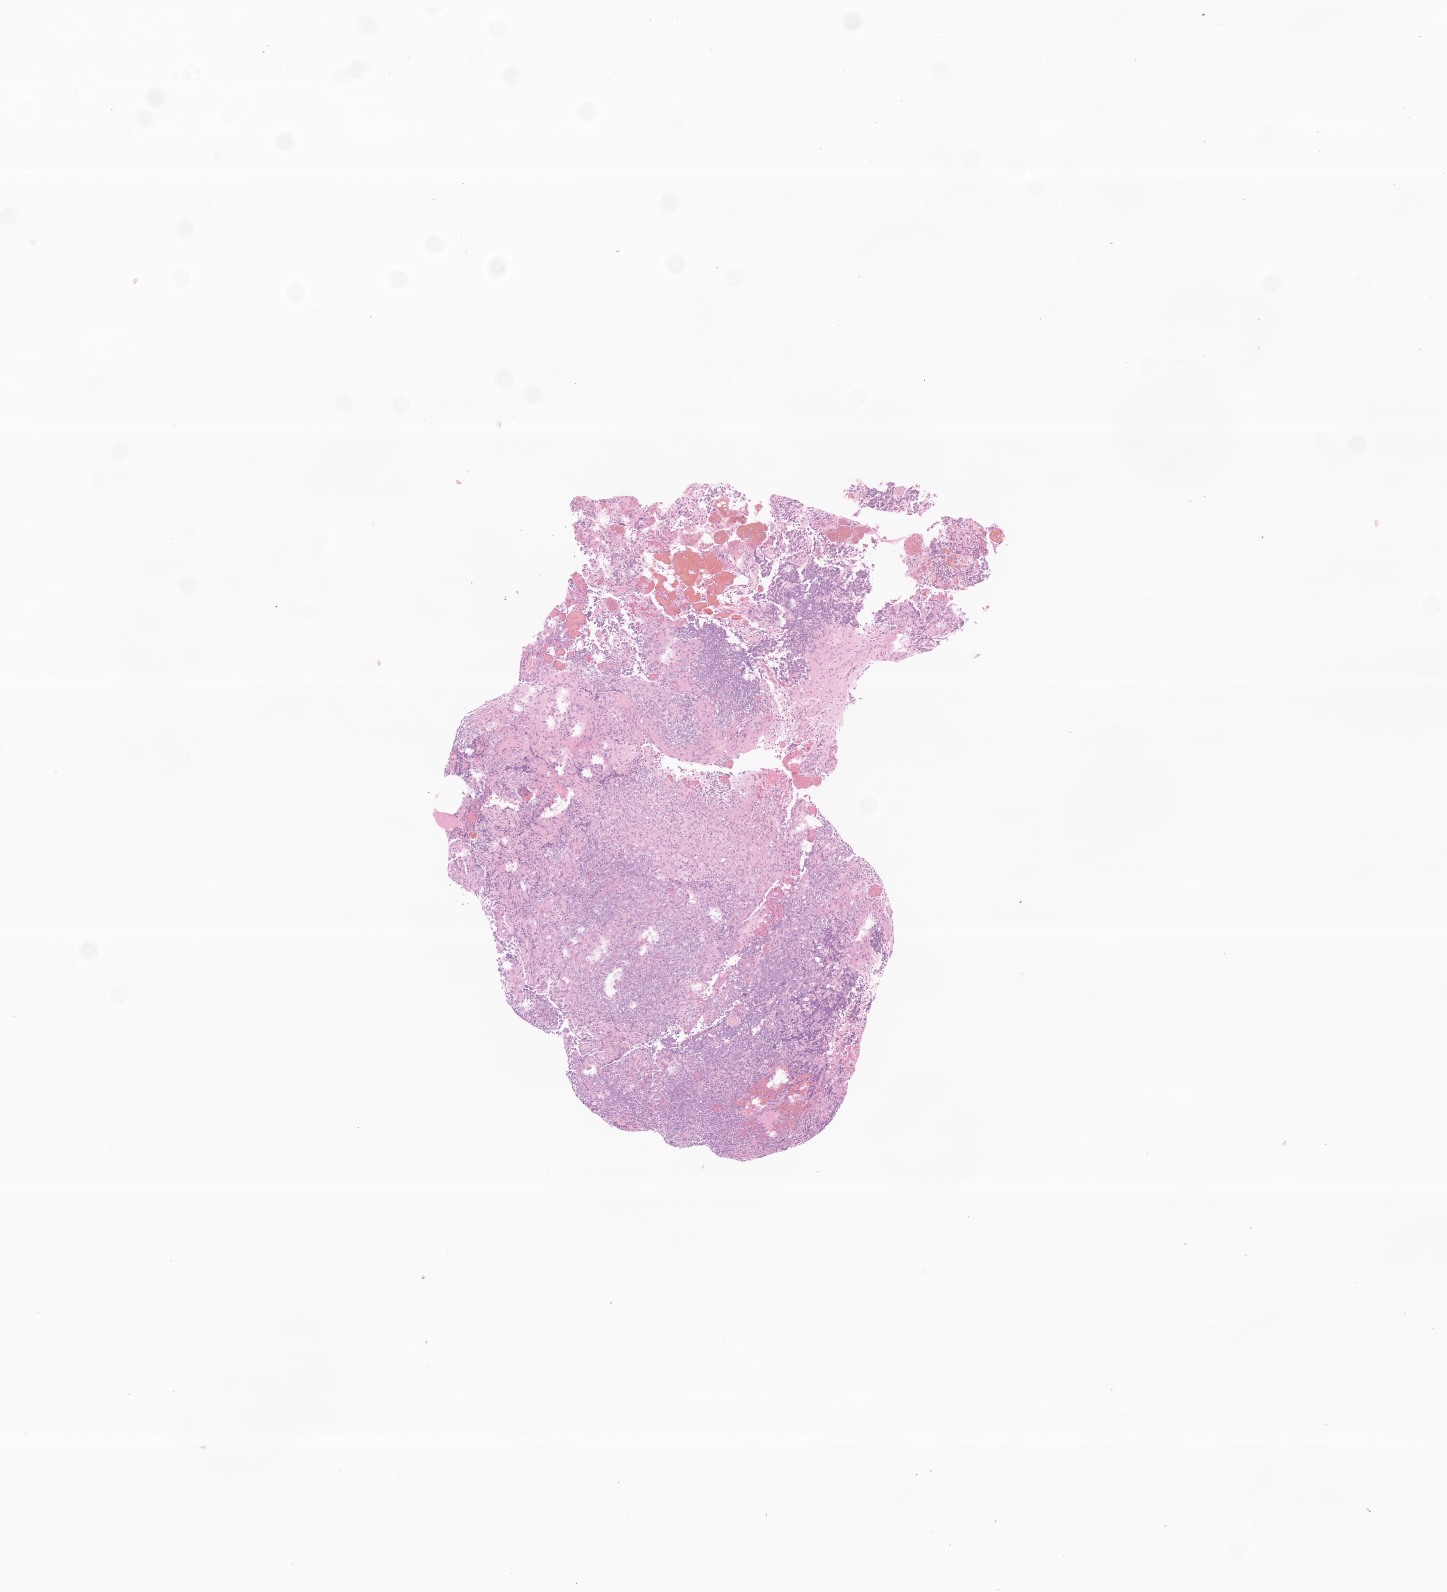
Whole-slide image, haematoxylin and eosin stain of tumor tissue from the cerebellum — a low-resolution overview of the entire scanned area, about 6.1 x 6.7 mm; formalin-fixed, paraffin-embedded (FFPE) tissue. Patient male; age 890 days (about 2.4 years).
Diagnosis (ICD-O-3 morphology term): Atypical teratoid/rhabdoid tumor.